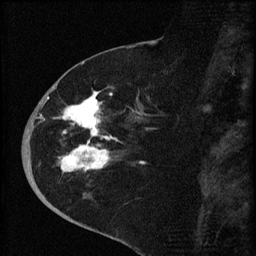
Breast MRI (dynamic contrast-enhanced), one sagittal slice. Position 29 of 60 along the scan axis. Dynamic contrast-enhanced series, image 2 of 4 at this slice position (ordered by acquisition). 1.5 T. TE 4.2 ms, TR 8.2 ms. 2 mm slice thickness. 256 × 256 image matrix. Female patient, age 71 years.
Structures marked on this image (semi-automatically segmented with operator editing):
- analysis volume of interest (the breast-tissue region the enhancement analysis was run in; not a lesion): box from (x=35, y=75) to (x=151, y=190) px
- tumour enhancement mask (voxels above the 70 % enhancement threshold inside the analysis volume of interest): (x=46, y=85)–(x=115, y=172)